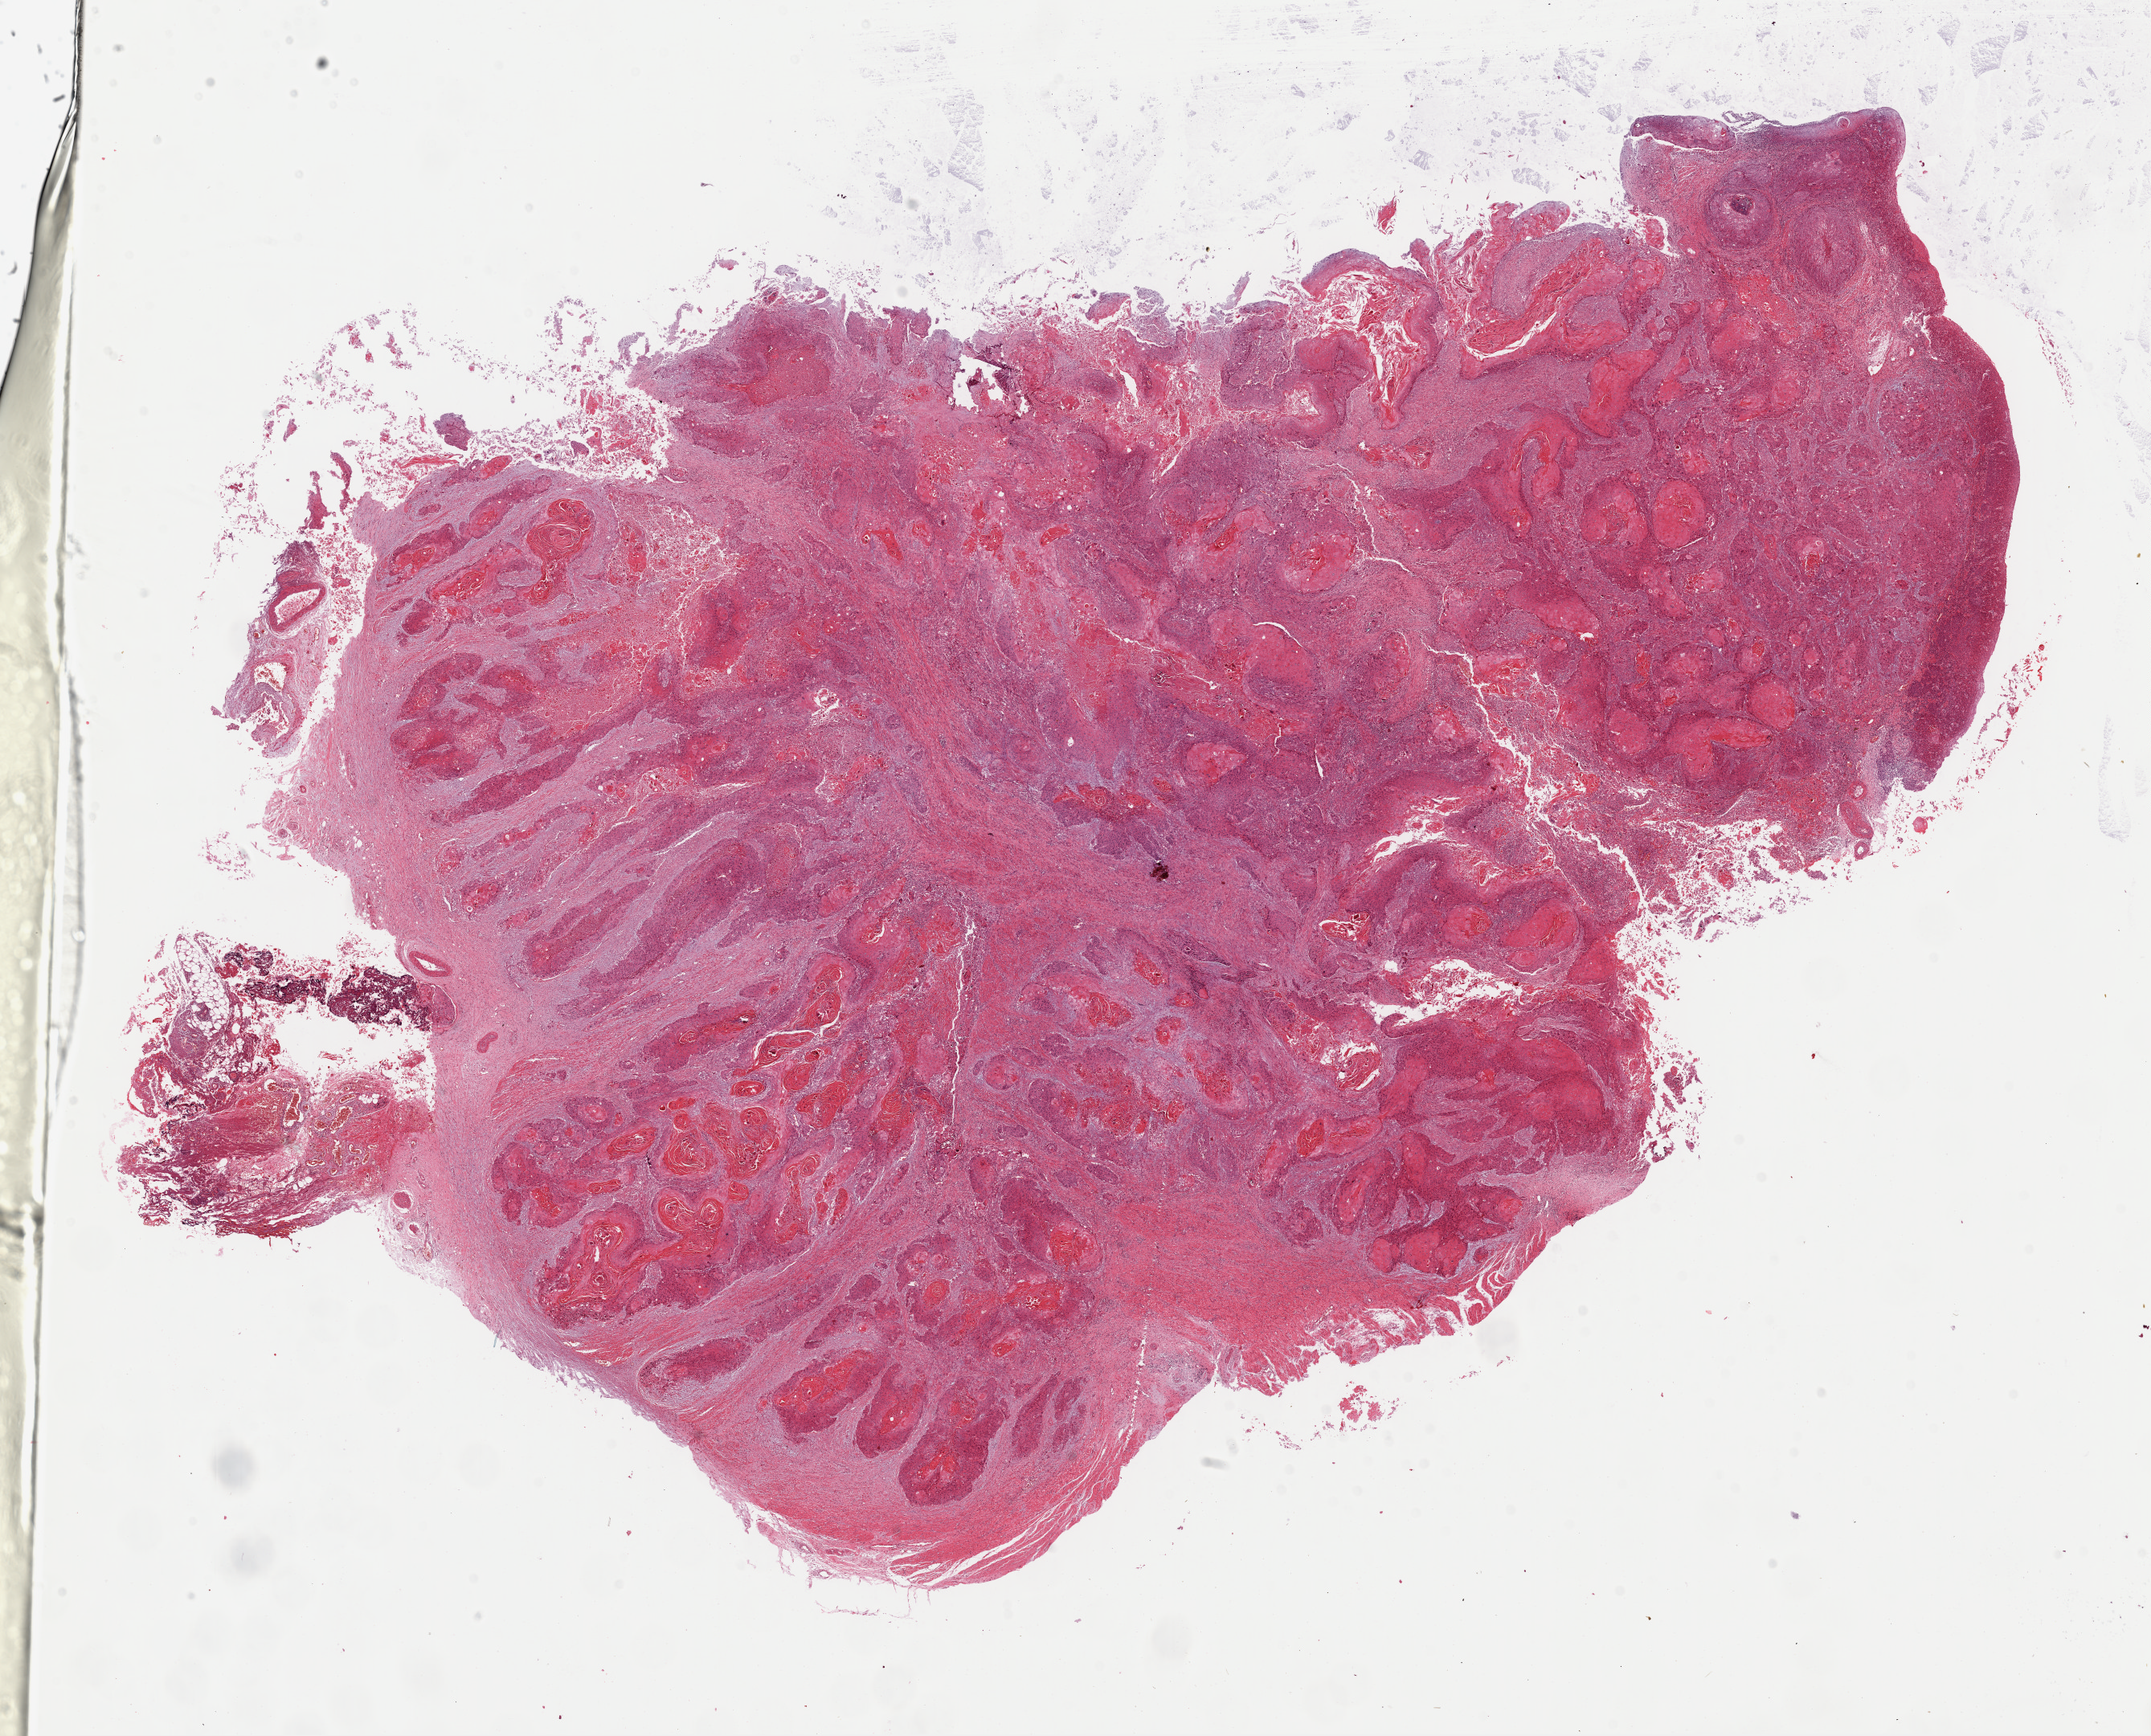
Whole-slide histology image, Hematoxylin and eosin (H&E) stained, a low-resolution overview of the entire scanned area, about 21.1 x 17.1 mm (acquisition: 40x scan), FFPE section, sample: primary tumour, esophagus. Patient: male, age at initial diagnosis 60 years.
Diagnosis: Squamous cell carcinoma, NOS.